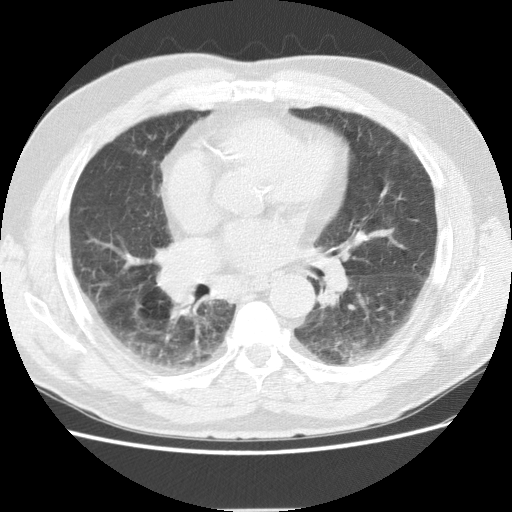
Chest CT (low-dose screening protocol), one axial image. Baseline annual screen. Lung window (W 1500 / L -600 HU). 2.5 mm slice thickness. Slice 65 of 155 in the series. Male, age 72 years at enrolment.
- Lesion marked by an expert reader, bounding box <149,240,194,276> (left, top, right, bottom; pixels).
- No non-calcified nodule or mass ≥4 mm was recorded by the screening reader at this exam.
- Official screen result: negative screen, minor abnormalities not suspicious for lung cancer.
- Lung cancer was diagnosed 163 days after this screen: adenocarcinoma, NOS, right middle lobe, stage IIIB (AJCC 6th edition), 27 mm at pathology.